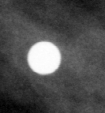
Region of interest cut from a scanned film mammogram (one marked finding); left breast; MLO view; BI-RADS breast density category 3 (scale 1–4).
Finding: calcifications, morphology lucent center; BI-RADS assessment category 2; subtlety rating 3 on a 1 (subtle) to 5 (obvious) scale; benign without callback (not worked up further).